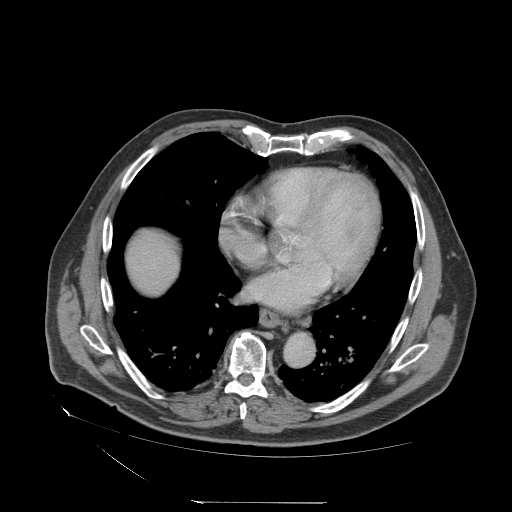
Contrast-enhanced abdominal CT (liver protocol), one axial slice; slice 74 of 83 in the series (ordered by position); reconstruction kernel STANDARD; soft-tissue window (W 400 / L 40 HU); 2.5 mm slice thickness; 512 × 512 image matrix. Case-level facts recorded for this patient, not image findings: diagnosis: hepatocellular carcinoma (patient treated with transarterial chemoembolisation; whether this scan precedes or follows treatment is not stated here); TNM stage (as recorded): Stage-I; Child-Pugh class: A; tumour nodularity: uninodular.
Outlined on this slice (semi-automatic segmentation, software-assisted and operator-edited):
- liver parenchyma outside the tumour (the mass and vessels are separate outlines, so this box may not span the whole liver): bounding box (x1, y1, x2, y2) in pixels: (126, 230, 178, 294)